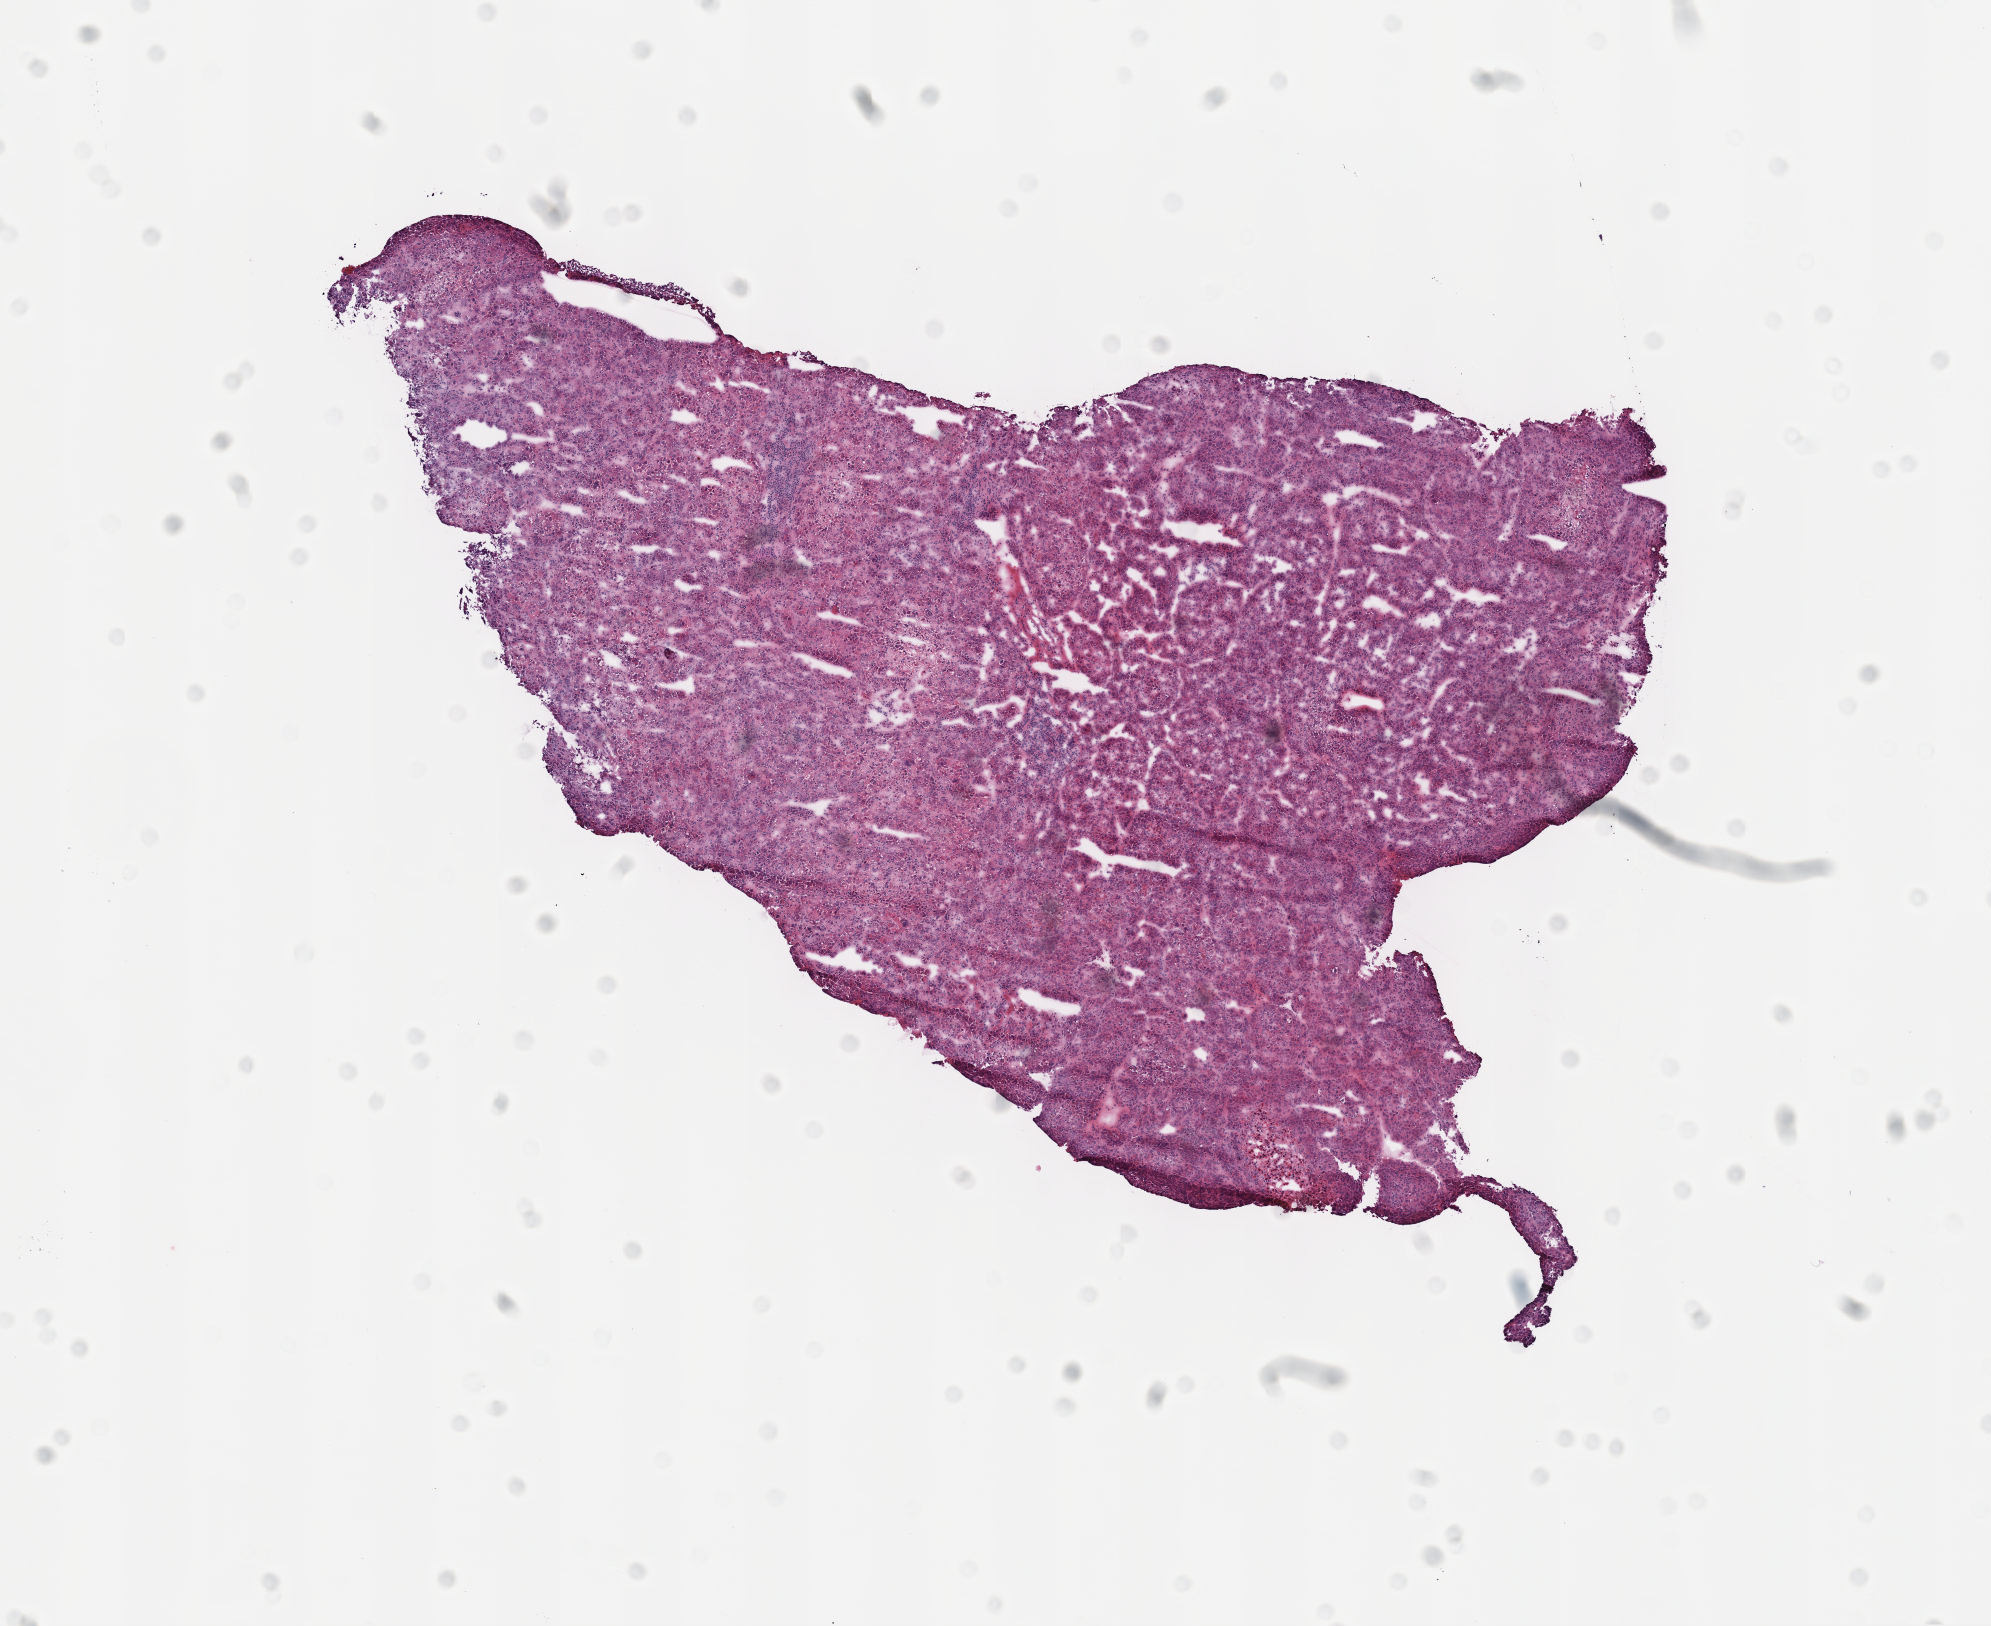
Whole-slide histology image, H&E — a low-resolution overview of the entire scanned area, about 8.1 x 6.6 mm (acquisition: 40x scan), frozen section, sample: primary tumour, liver. Male patient; age at initial diagnosis 51 years. Slide review estimates, as recorded: tumour cells 90%, tumour nuclei 95%.
Diagnosis: Hepatocellular carcinoma, NOS.